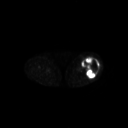
FDG PET of an extremity soft-tissue mass (from a PET/CT study), one axial slice. Position 220 of 267 along the scan axis. 3.27 mm slice thickness. 128 × 128 image matrix, field of view 700 × 700 mm. Female patient, age 62 years. Case-level facts recorded for this patient, not image findings: histological type: undifferentiated – high grade; grade: high; site of the primary tumour: left thigh.
Outlined on this slice (expert contour drawn on MRI and transferred to this co-registered scan by the dataset authors):
- gross tumour volume including surrounding oedema: bounding box <82,56,100,78> (left, top, right, bottom; pixels)
- gross tumour volume (mass): <82,56,100,78>